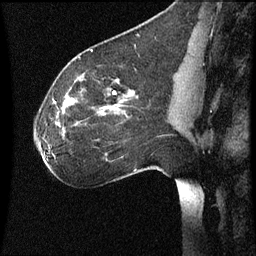
Breast MRI (dynamic contrast-enhanced), one sagittal slice; position 39 of 60 along the scan axis; dynamic contrast-enhanced series, image 2 of 3 at this slice position (ordered by acquisition); 1.5 T; TE 4.2 ms, TR 8.9 ms; 2 mm slice thickness; 256 × 256 image matrix, field of view 200 × 200 mm. Patient: female, 35 years. Case-level facts recorded for this patient, not image findings: setting: breast cancer imaged before/during neoadjuvant chemotherapy; receptor status: HER2-positive.
Outlined on this slice (semi-automatic segmentation, software-assisted and operator-edited):
- analysis volume of interest (the breast-tissue region the enhancement analysis was run in; not a lesion): bounding box [x1, y1, x2, y2] px = [32, 66, 177, 177]
- tumour enhancement mask (voxels above the 70 % enhancement threshold inside the analysis volume of interest): [69, 102, 75, 107]